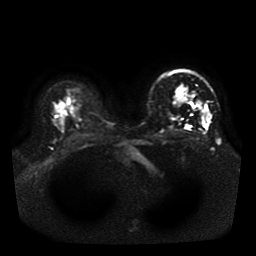
Breast MRI, one axial slice. Position 30 of 41 along the scan axis. Diffusion-weighted series; image 2 of 4 stored at this slice position (different b-values; order by instance number). 1.5 T. 256 × 256 image matrix, field of view 330 × 330 mm. Female patient.
Outlined on this slice (expert manual segmentation):
- tumour on diffusion-weighted imaging: bounding box [x1, y1, x2, y2] px = [205, 112, 211, 125]